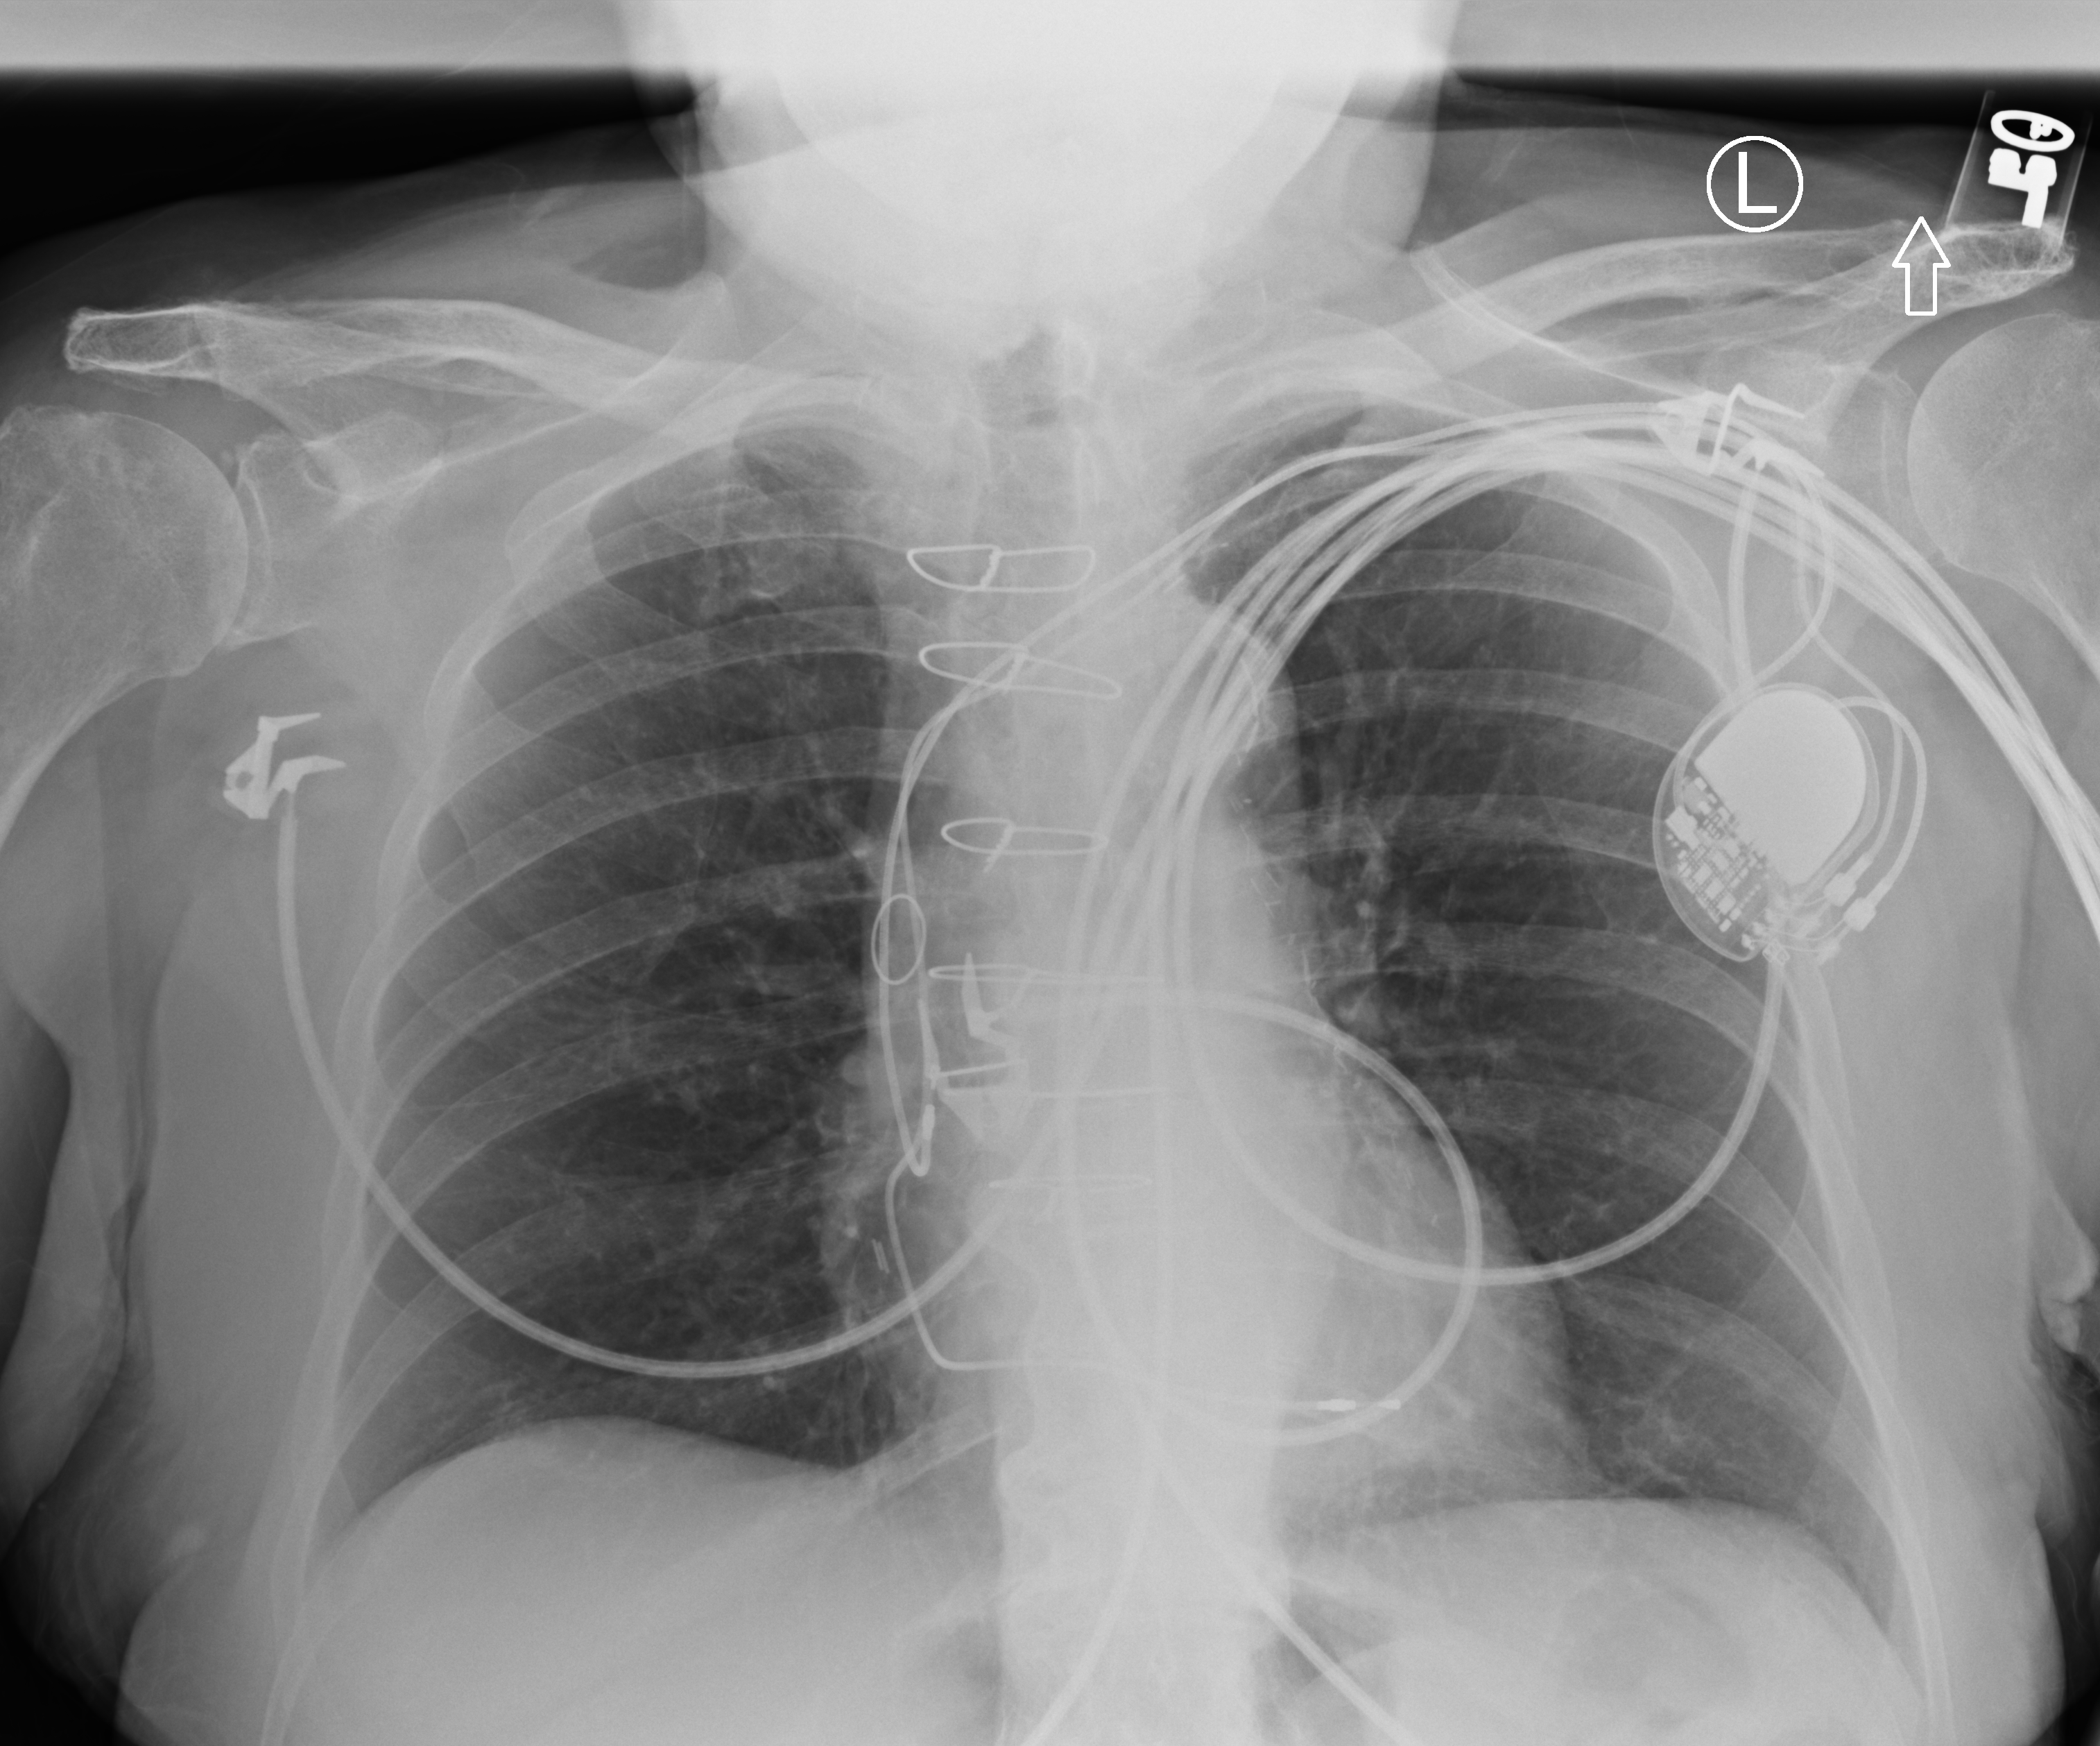
Chest X-ray (portable); anteroposterior (AP) projection. Patient hospitalised with COVID-19; female, aged 75–90 years.
Admission-level facts for this patient (not findings on this image; timing relative to this image not recorded): mechanically ventilated during this hospital stay: no.